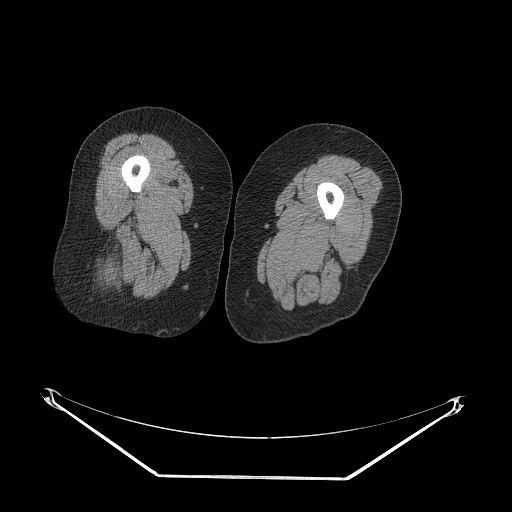
CT of an extremity soft-tissue mass (from a PET/CT study), one axial slice. Position 24 of 257 along the scan axis. Reconstruction kernel STANDARD. 140 kVp. Soft-tissue window (W 400 / L 40 HU). 3.75 mm slice thickness. 512 × 512 image matrix, field of view 500 × 500 mm. Female patient. Case-level facts recorded for this patient, not image findings: histological type: synovial sarcoma; grade: intermediate; site of the primary tumour: right buttock.
Structures marked on this image (expert contour drawn on MRI and transferred to this co-registered scan by the dataset authors):
- gross tumour volume including surrounding oedema: bounding box [x1, y1, x2, y2] px = [96, 240, 118, 287]